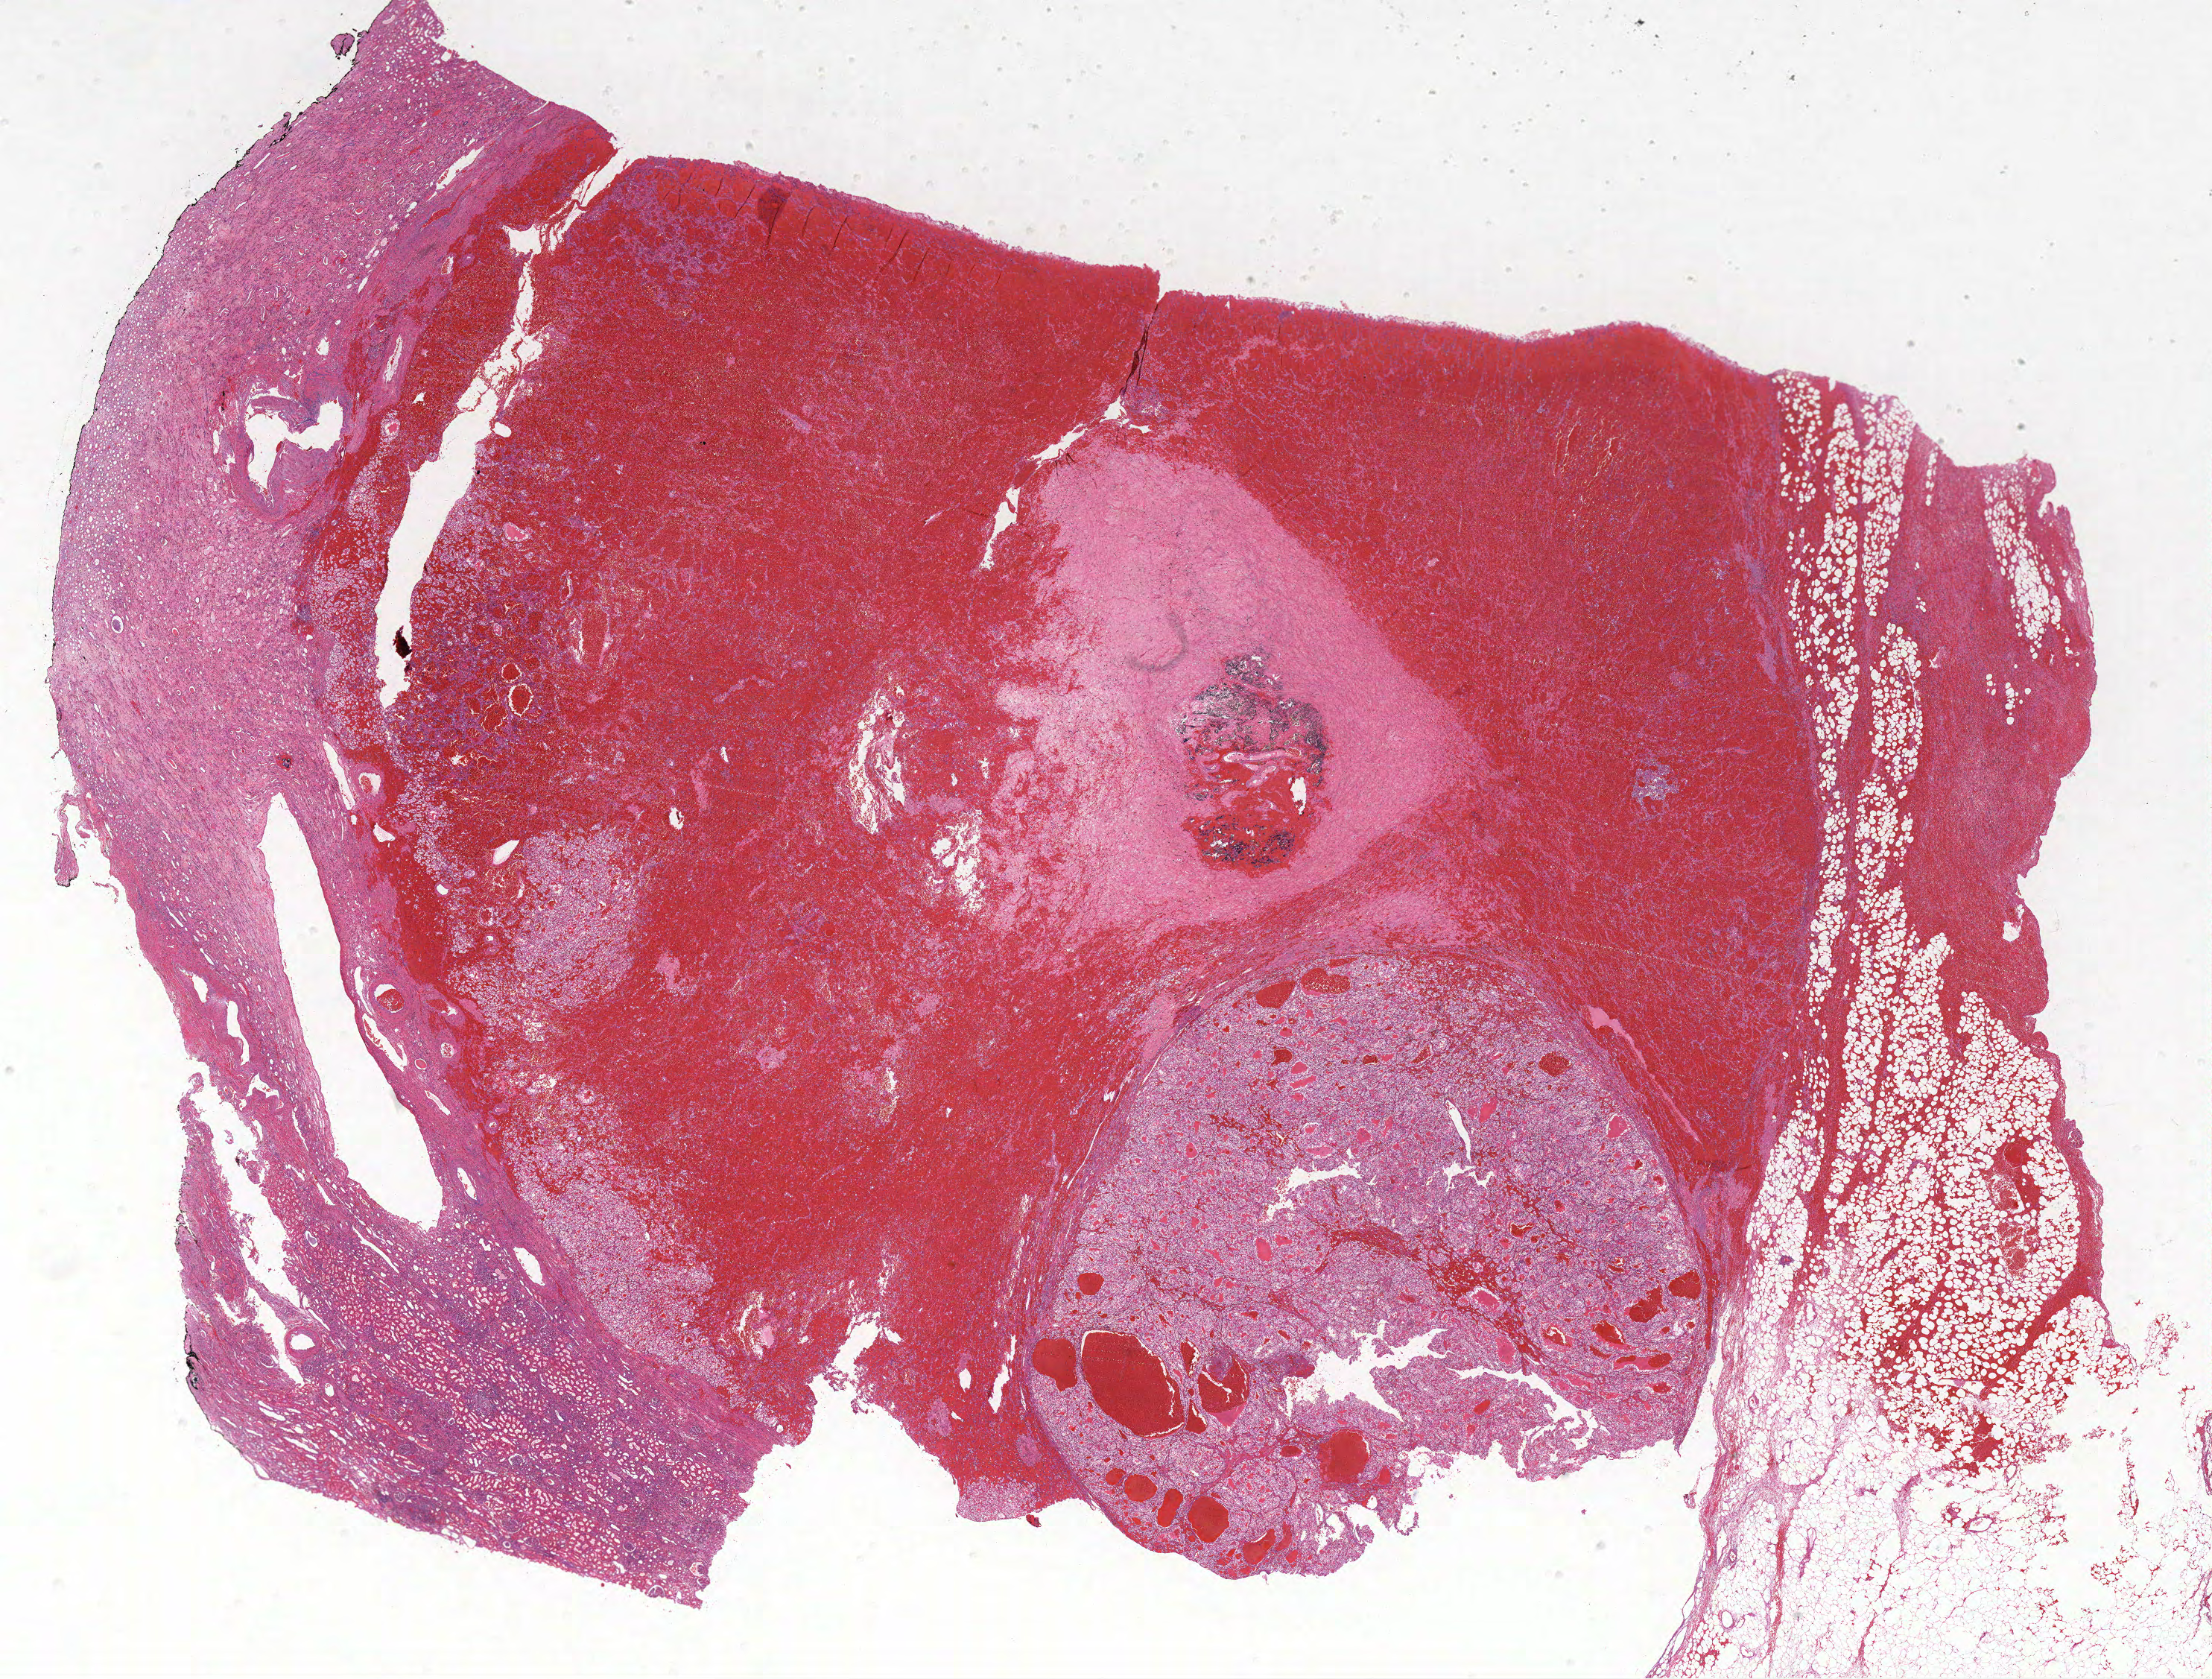
Whole-slide histology image, Hematoxylin and eosin (H&E) stained, a low-resolution overview of the entire scanned area, about 23.7 x 18.0 mm; FFPE section; primary tumour sample from the kidney. Male, age 75 years at initial diagnosis. Histologic grade: G2 (moderately differentiated).
AJCC pathologic stage: III. TNM: T3a NX M0. Pathologic diagnosis: Clear cell adenocarcinoma, NOS.